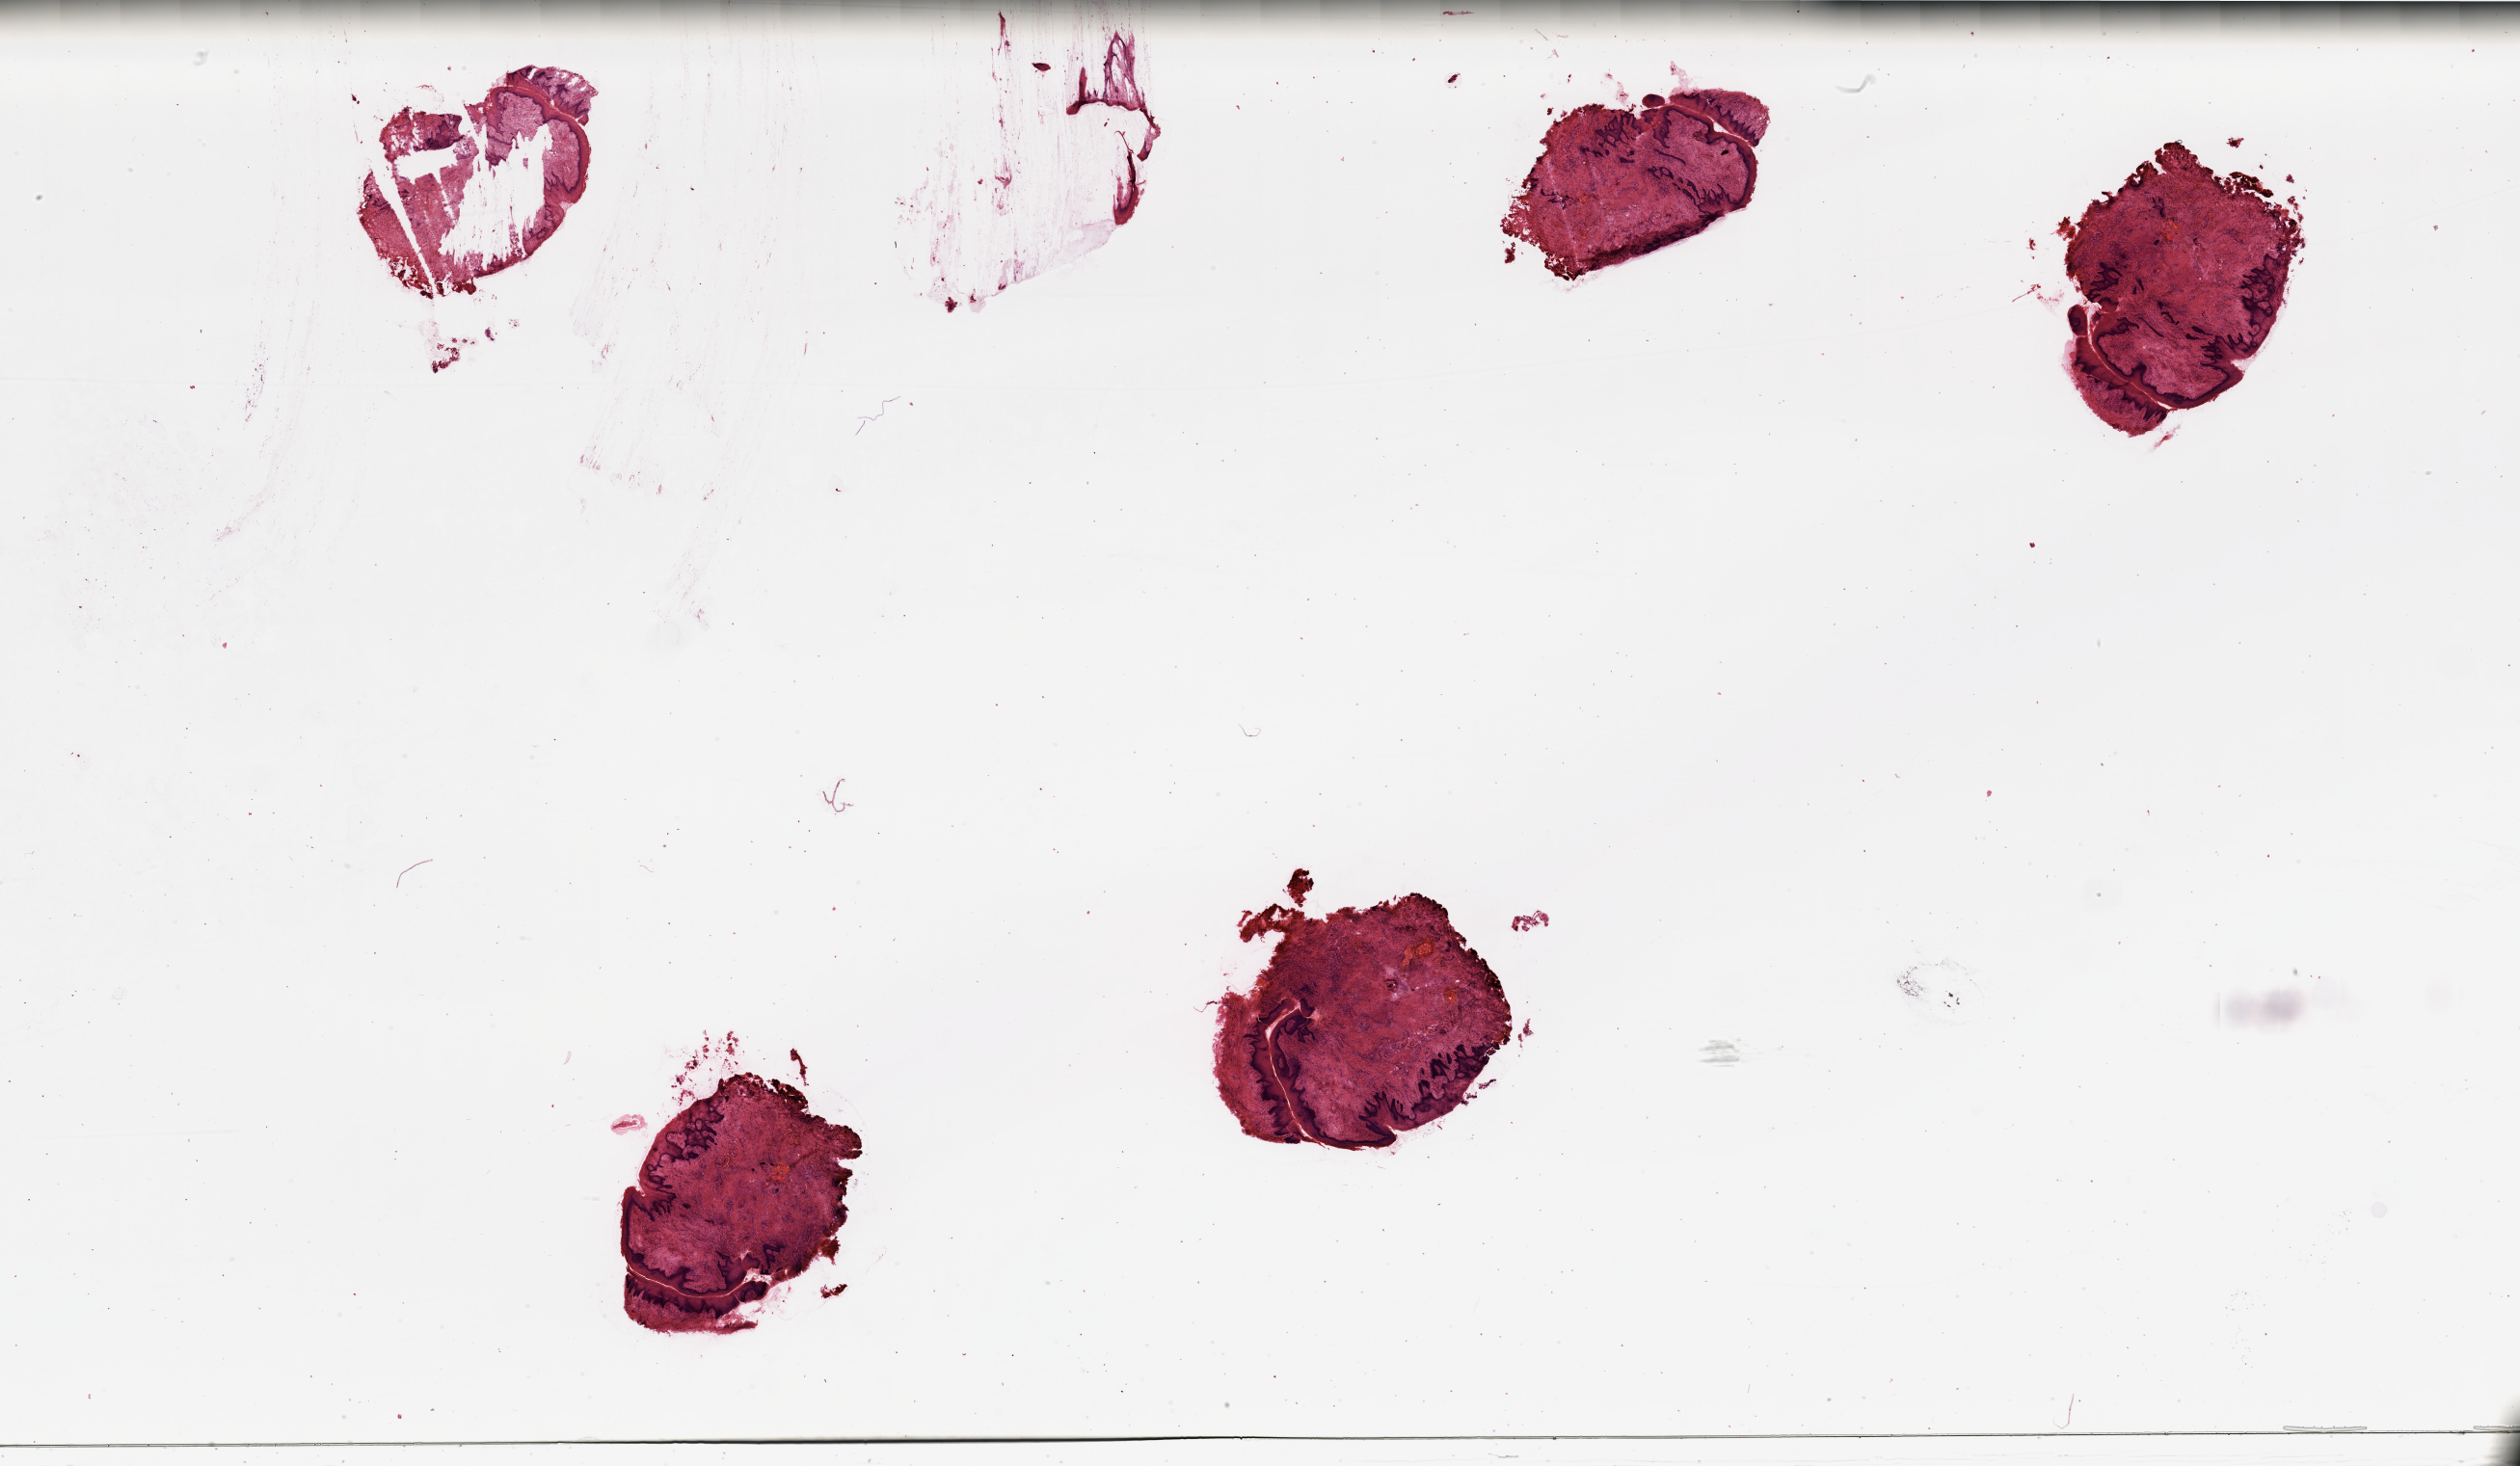
Whole-slide histology image, Hematoxylin and eosin (H&E) stained, shown as a low-resolution overview of the whole scanned area (about 41.3 x 24.1 mm), head and neck, normal (non-tumour) tissue. Patient: male, age 53 years.
- this section: normal (non-tumour) tissue from the same patient
- patient diagnosis: Squamous cell carcinoma, NOS (tongue, NOS)